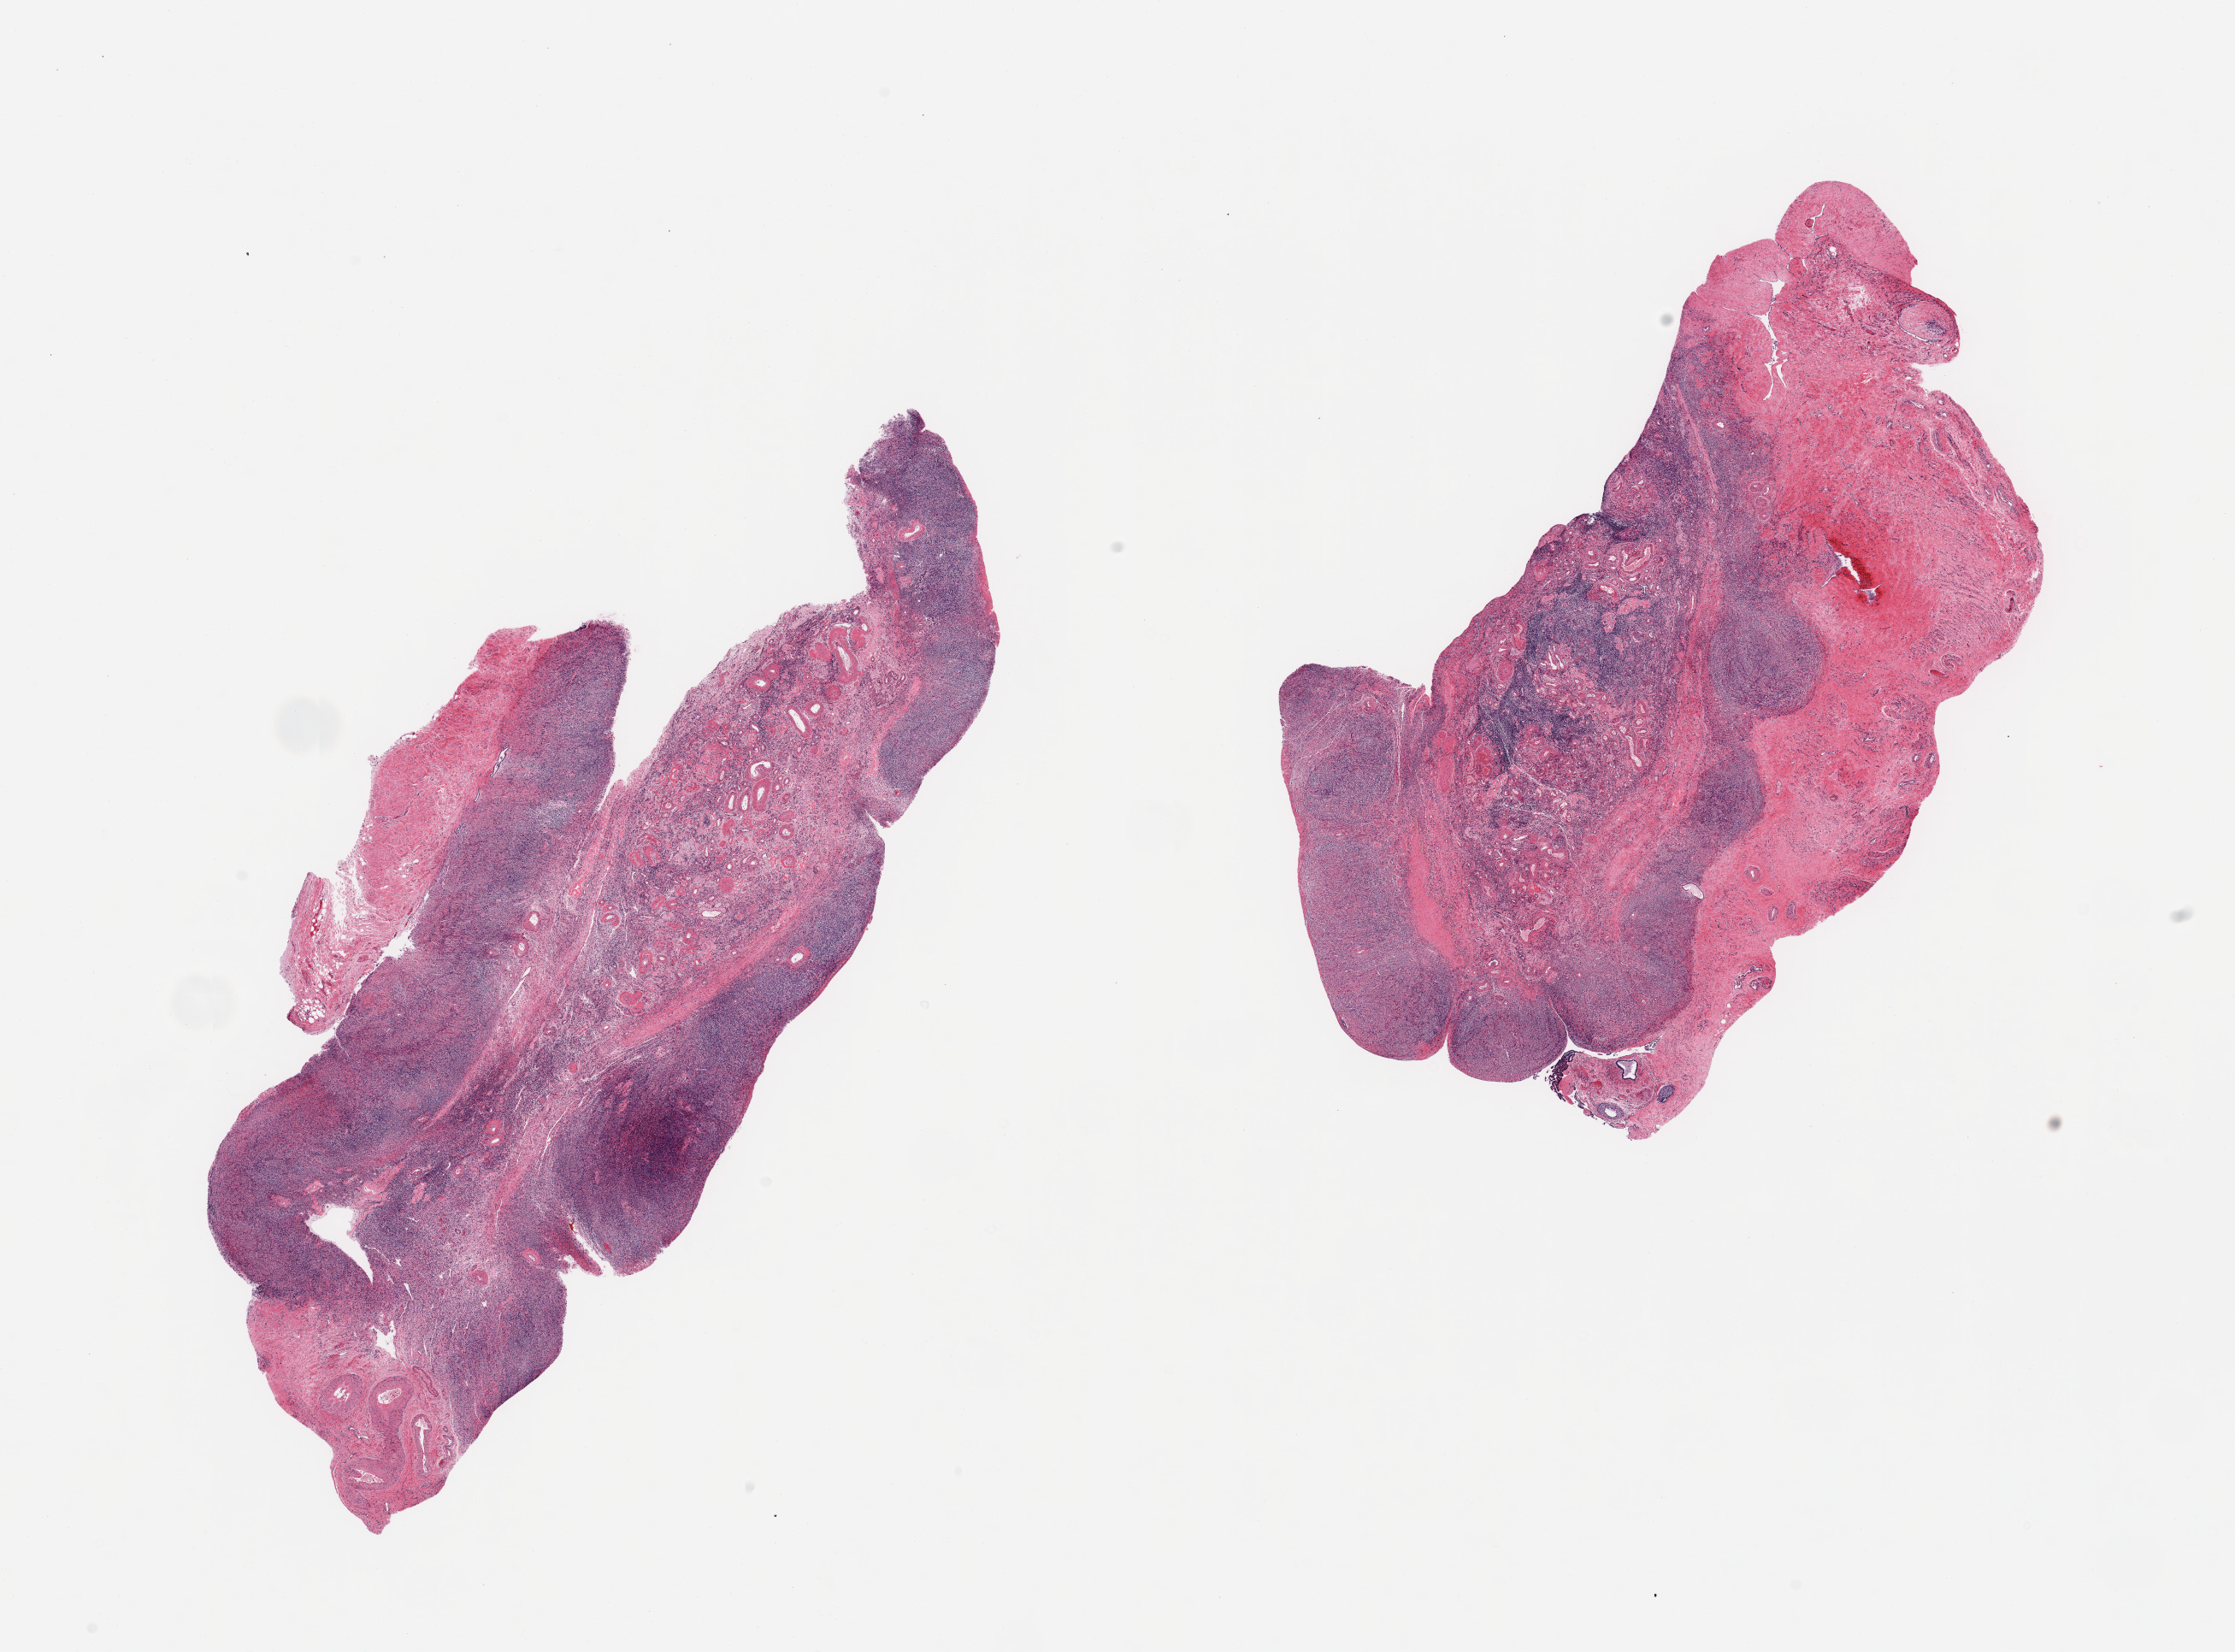
Whole-slide image, haematoxylin and eosin stain, brightfield, whole scanned area (about 20.7 x 15.3 mm) shown as a low-resolution overview; PAXgene-fixed, paraffin-embedded tissue; target tissue: ovary; donor tissue sample. Donor sex: female.
Review note (as recorded): 2 pieces; atrophic with 50% external fibrous content in 1 piece.